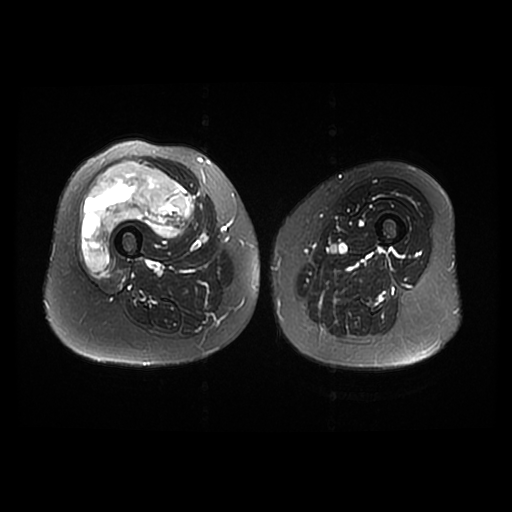
MRI of an extremity soft-tissue mass, one axial slice; slice 17 of 42 in the series (ordered by position); T2-weighted fat-saturated; 6 mm slice thickness; 512 × 512 image matrix, field of view 440 × 440 mm. Female patient. From the clinical record (not read from this slice): histological type: pleiomorphic undifferentiated sarcoma; grade: high; site of the primary tumour: right quadricep.
Outlined on this slice (outlined manually by an expert reader):
- gross tumour volume including surrounding oedema: bounding box [x1, y1, x2, y2] px = [81, 161, 194, 272]
- gross tumour volume (mass): [81, 161, 194, 272]